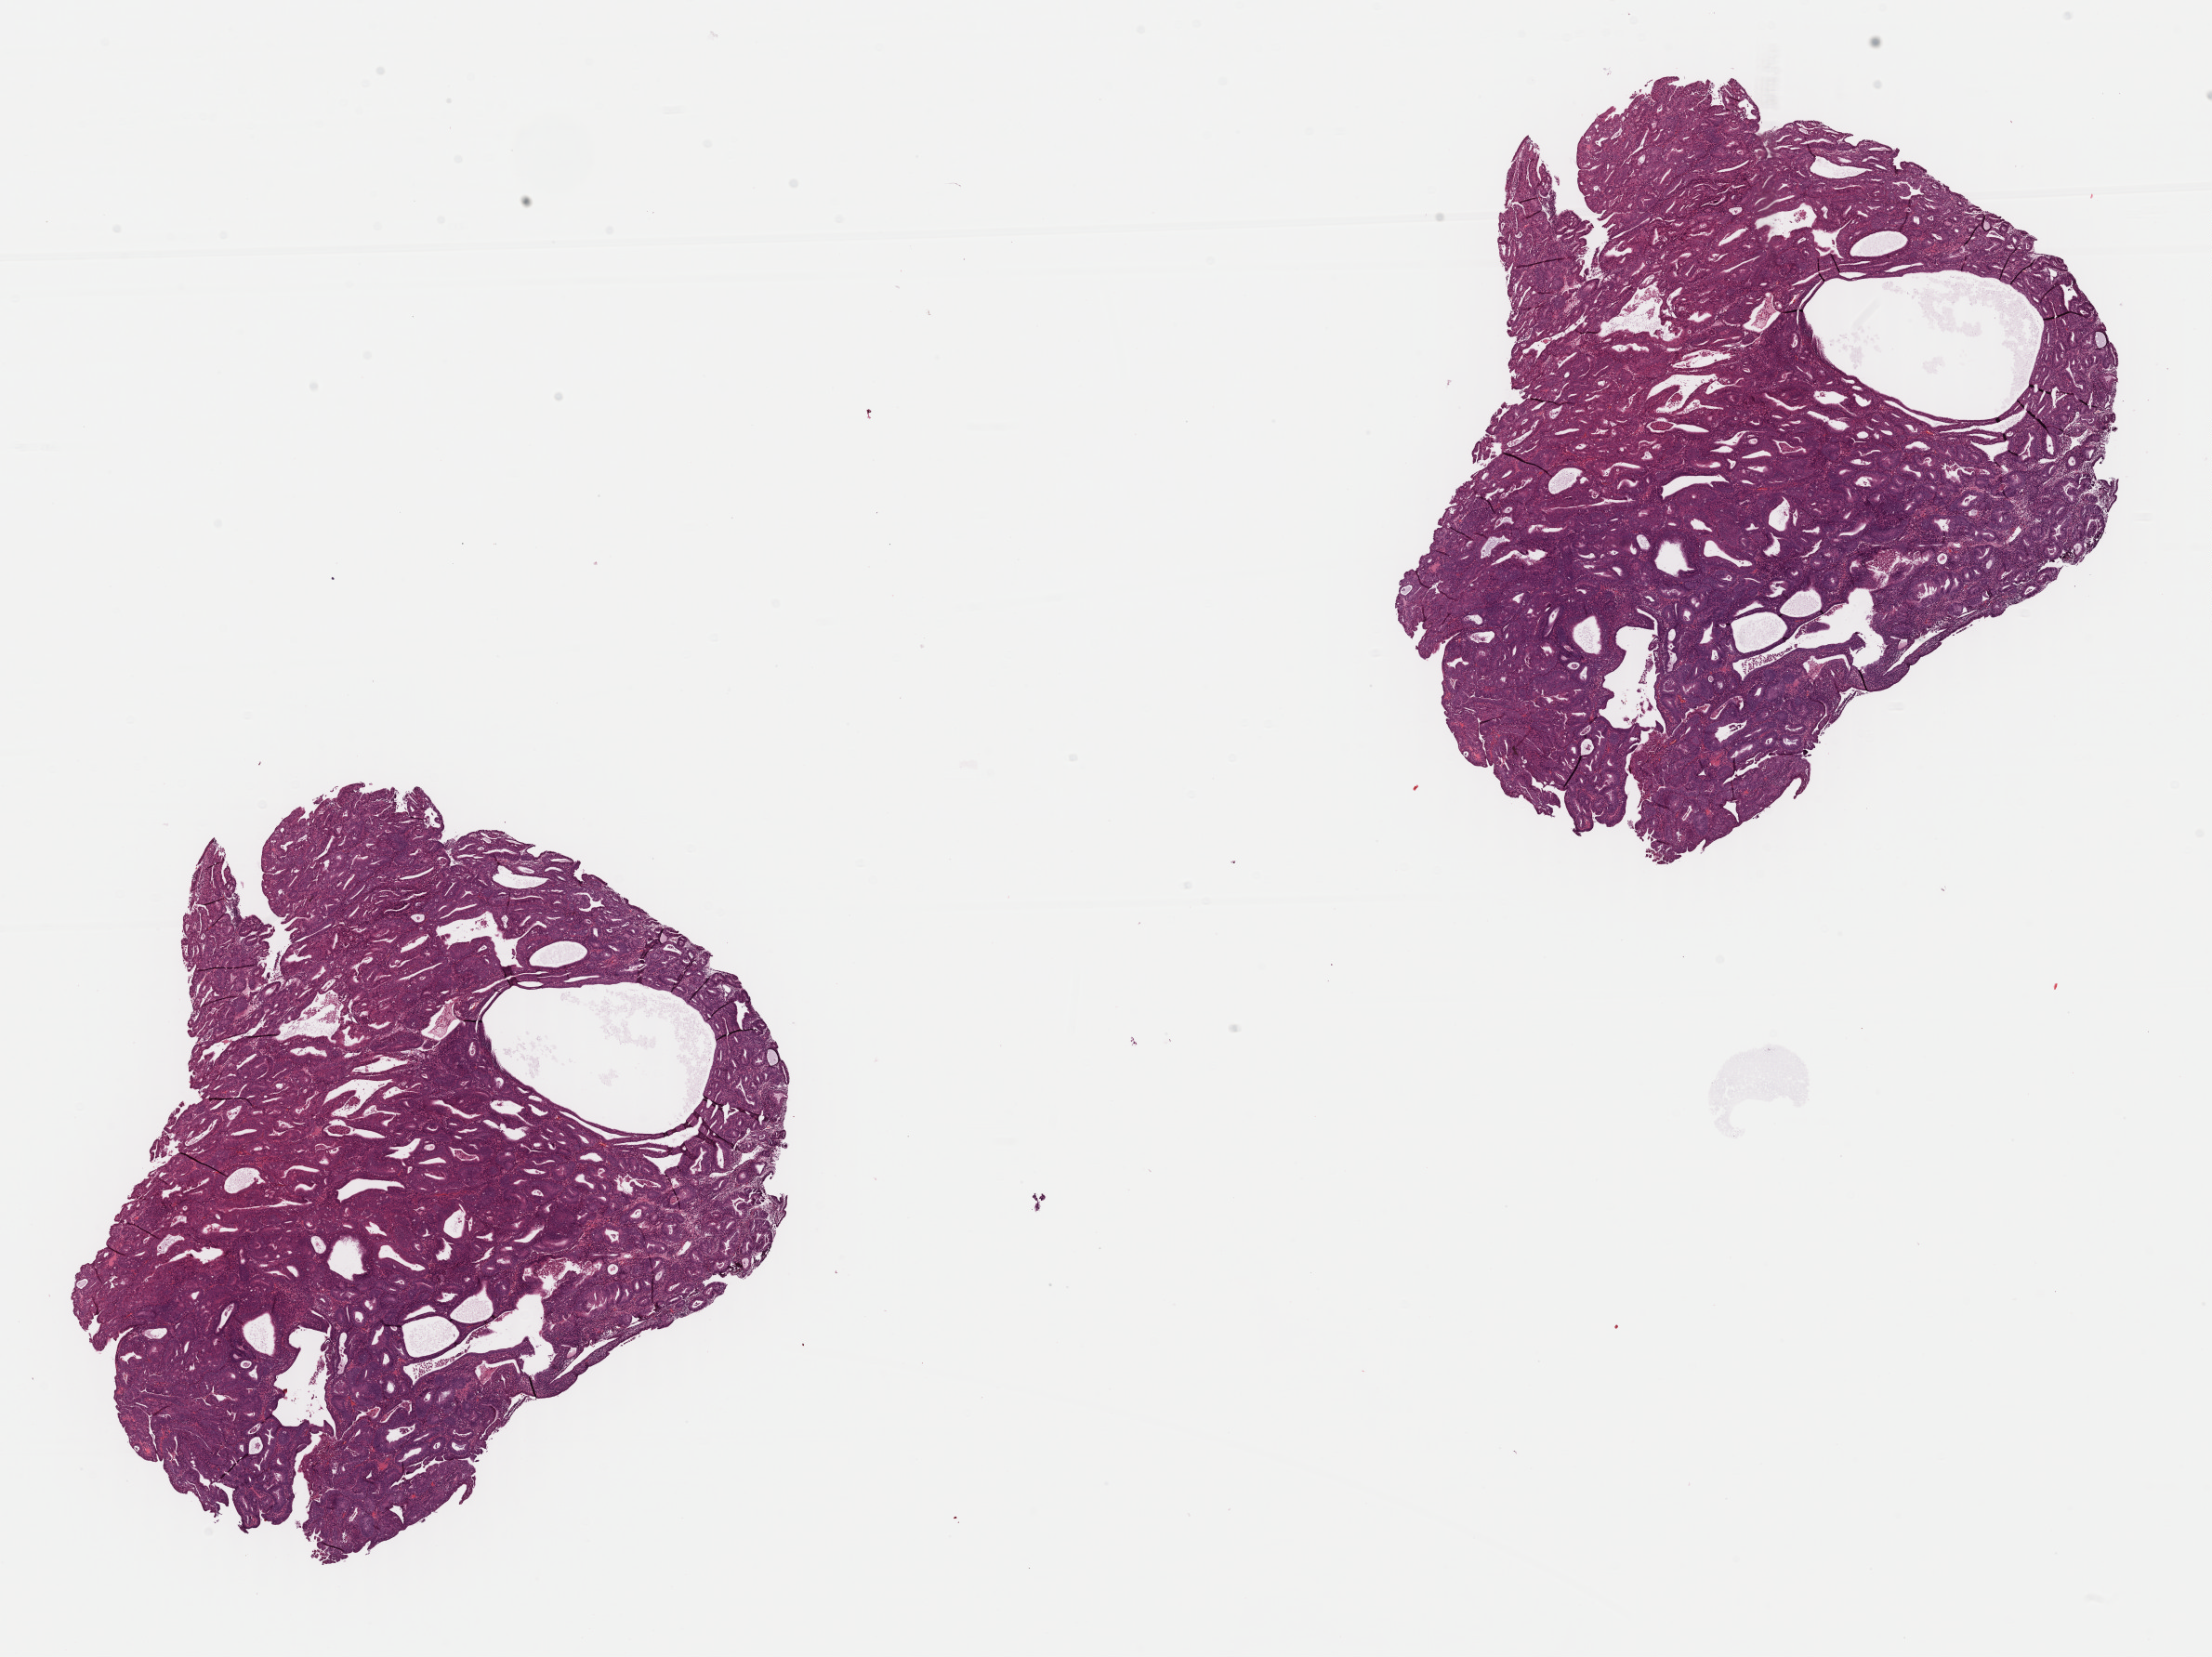
Digitized H&E tissue section (whole slide) — low-resolution overview of the scanned area, about 18.8 x 14.1 mm, formalin-fixed paraffin-embedded (FFPE) diagnostic section, primary tumour sample from the uterus. Patient: female, age at initial diagnosis 61 years. Histologic grade: G3 (poorly differentiated).
* FIGO stage: IIIC
* histologic diagnosis: Serous cystadenocarcinoma, NOS (endometrium)
* lymph nodes positive (case pathology): 9 of 14 examined